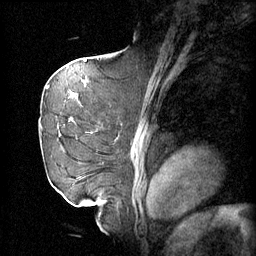
Breast MRI (dynamic contrast-enhanced), one sagittal slice; slice 37 of 60 in the series (ordered by position); 4 images stored at this slice position (order not interpretable as contrast timing); 1.5 T; TE 4.2 ms, TR 11 ms; 2 mm slice thickness; 256 × 256 image matrix. Patient: female, 72 years.
Structures marked on this image (semi-automatic segmentation, software-assisted and operator-edited):
- analysis volume of interest (the breast-tissue region the enhancement analysis was run in; not a lesion): bounding box (x1, y1, x2, y2) in pixels: (46, 68, 105, 163)
- tumour enhancement mask (voxels above the 70 % enhancement threshold inside the analysis volume of interest): (71, 68, 93, 107)